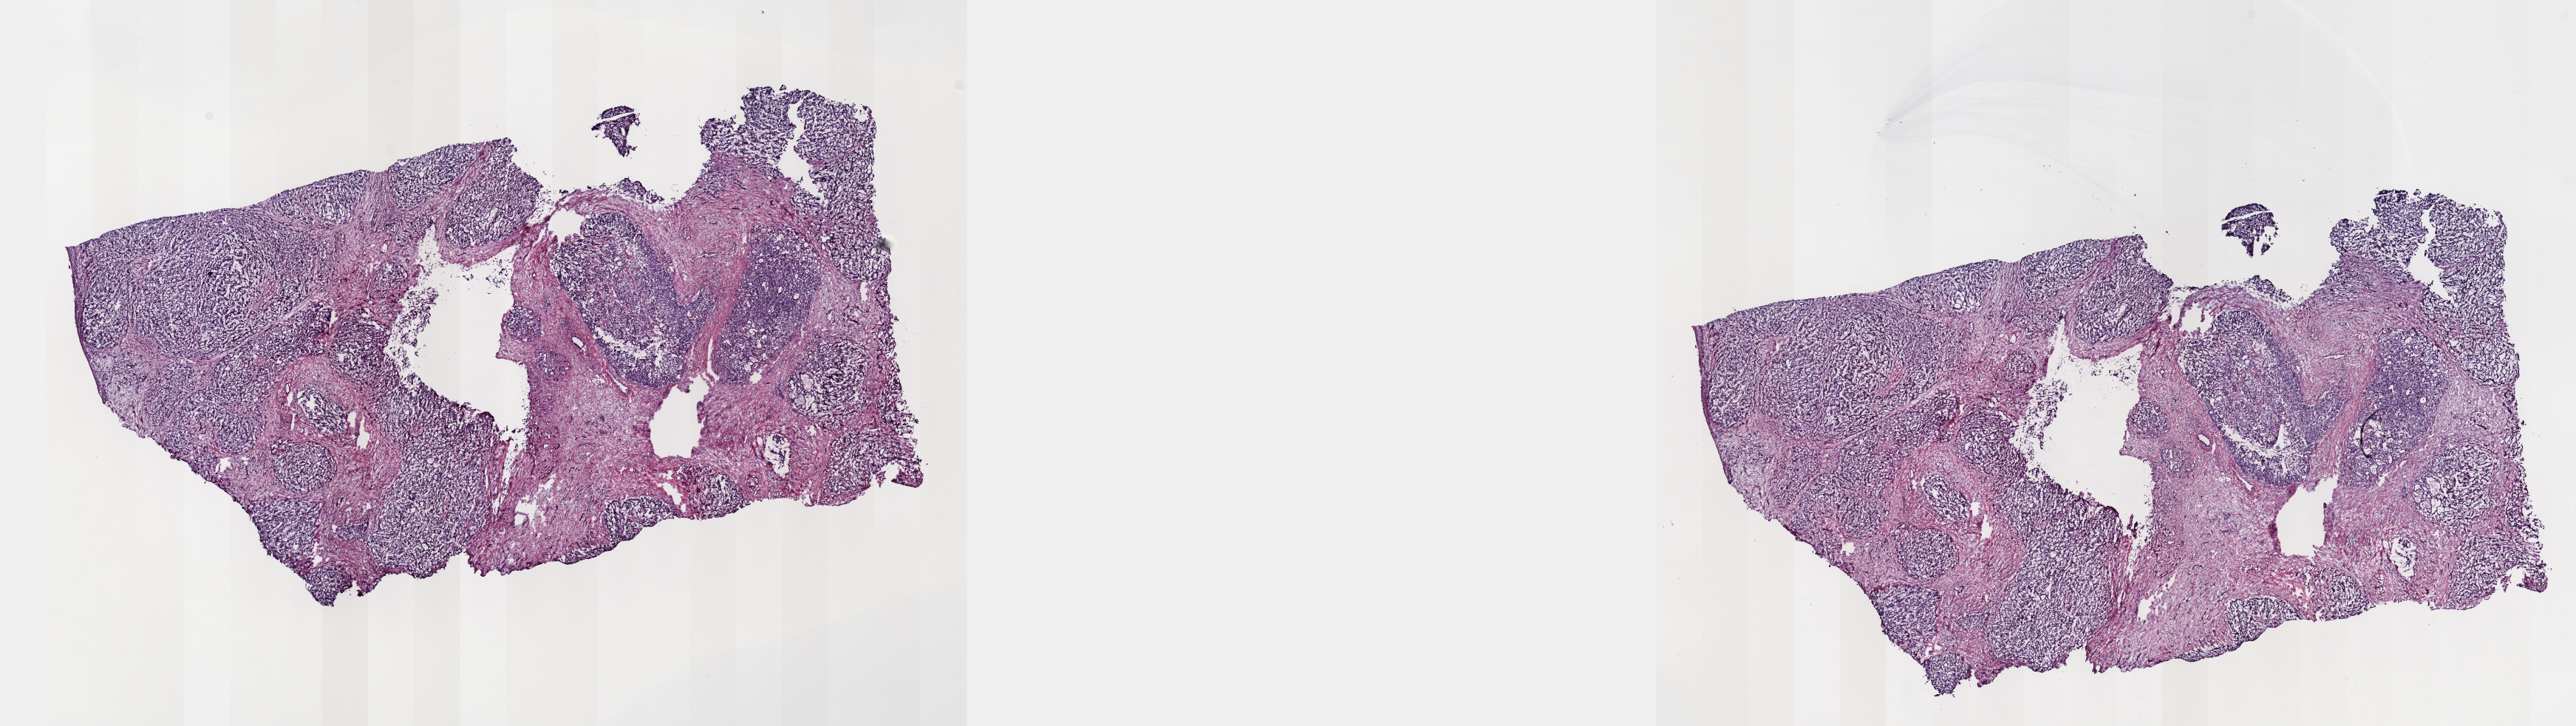
Whole-slide histology image, H&E-stained, low-resolution overview of the scanned area, about 28.2 x 7.9 mm (from a 40x scan). Frozen section from the top of the tissue portion. Sample: primary tumour, liver. Patient: male, age at initial diagnosis 61 years. Histologic grade: G2 (moderately differentiated). Pathologist review of this section (percent, as recorded): tumour cells 100%, tumour nuclei 65%, normal cells 0%, stromal cells 0%, necrosis 0%. Infiltration values recorded for this section: lymphocyte infiltration 2%, monocyte infiltration 0%, neutrophil infiltration 0%.
Diagnosis: Combined hepatocellular carcinoma and cholangiocarcinoma. AJCC pathologic stage: II.